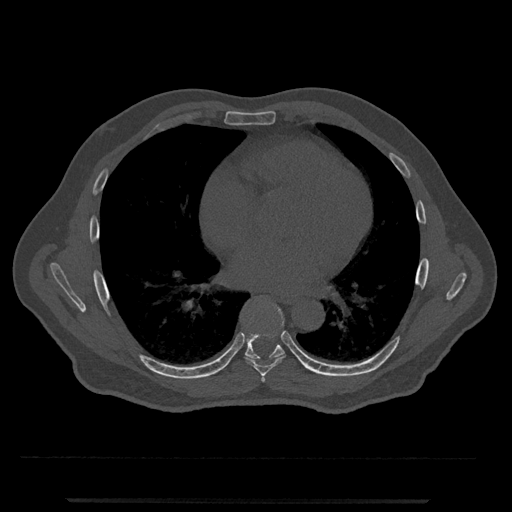
CT including the spine, one axial slice; slice 658 of 797 in the series (ordered by position); reconstruction kernel Br40s/3; bone window (W 1800 / L 400 HU); 0.5 mm slice thickness; 512 × 512 image matrix. Male patient, age 63 years. From the clinical record (not read from this slice): primary cancer: prostate.
Structures marked on this image (semi-automatically segmented with operator editing):
- T6 vertebra: bounding box (x1, y1, x2, y2) in pixels: (262, 376, 265, 382)
- T7 vertebra: (246, 325, 285, 377)
- T8 vertebra: (245, 311, 285, 361)